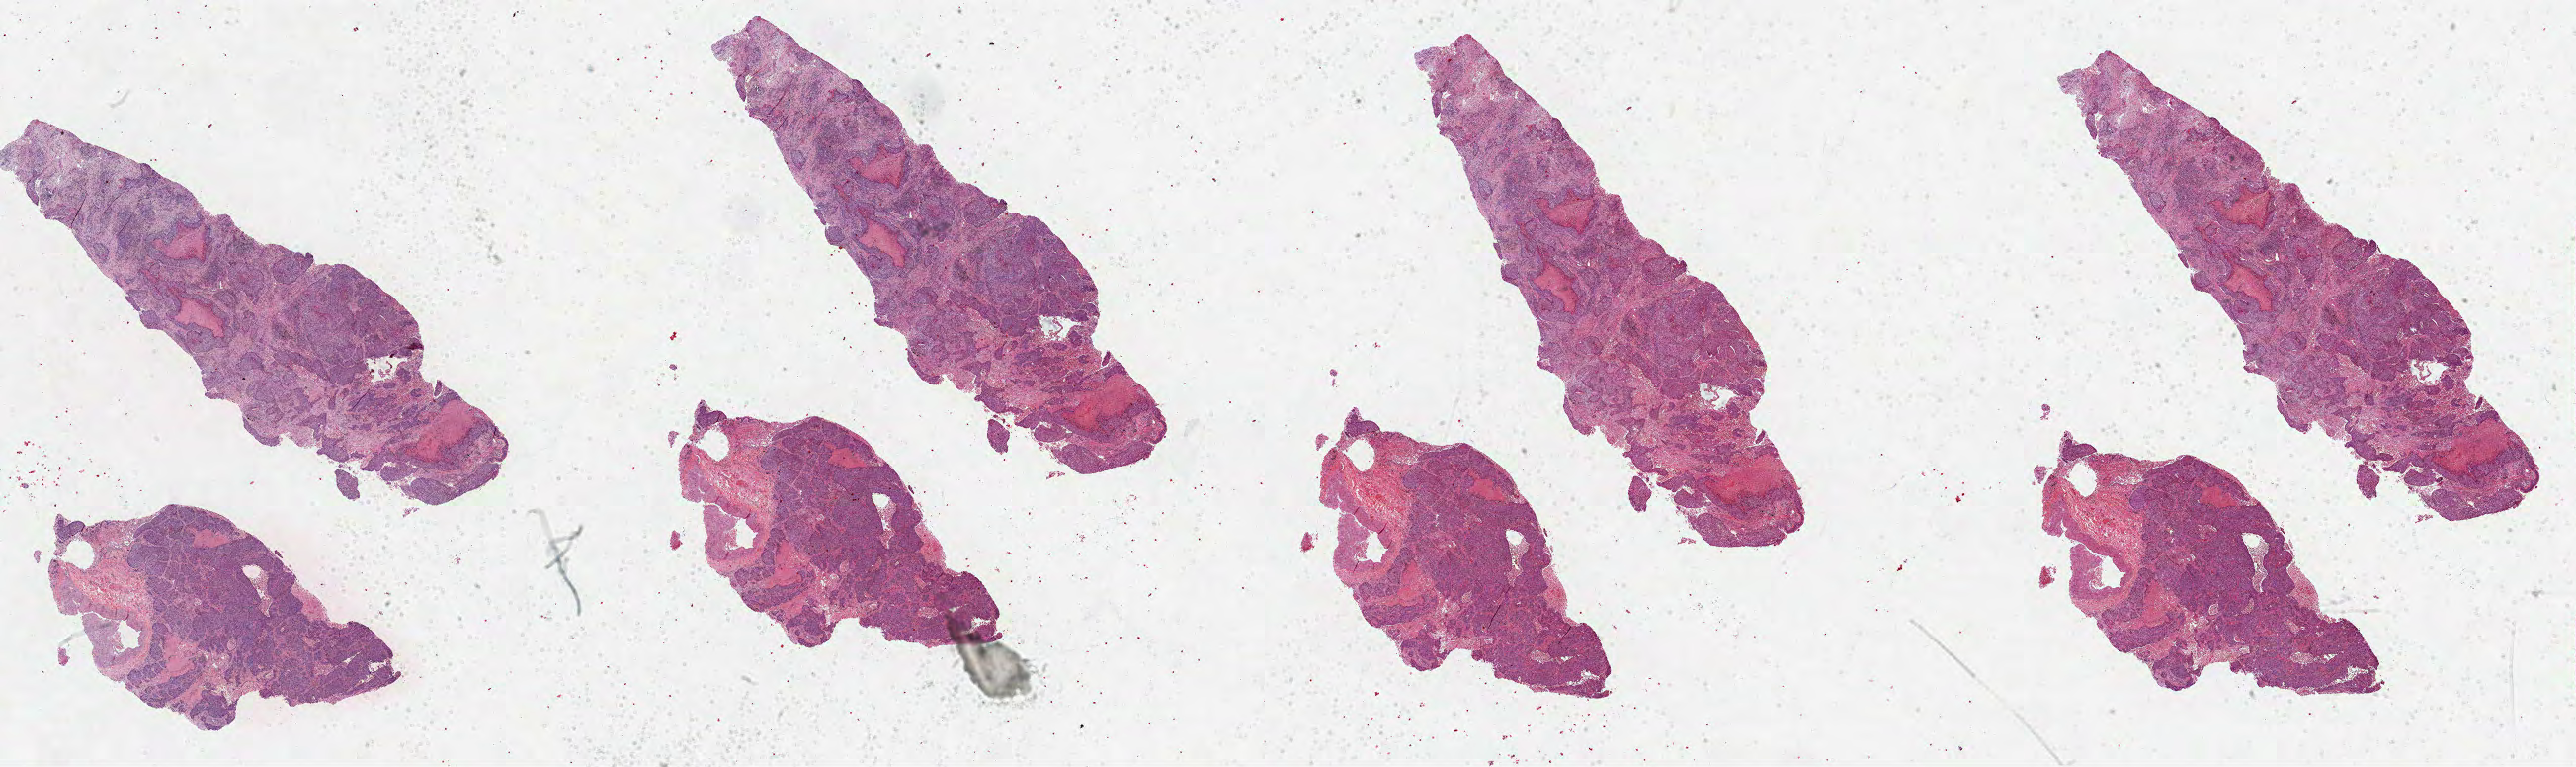
Hematoxylin and eosin (H&E) stained whole-slide image, whole scanned area (about 42.1 x 12.5 mm, acquisition: 40x scan) shown as a low-resolution overview; FFPE section; lung, primary tumour sample. Male, age 52 years at initial diagnosis.
- diagnosis: Squamous cell carcinoma, NOS (lower lobe, lung)
- AJCC pathologic stage: IB (6th edition)